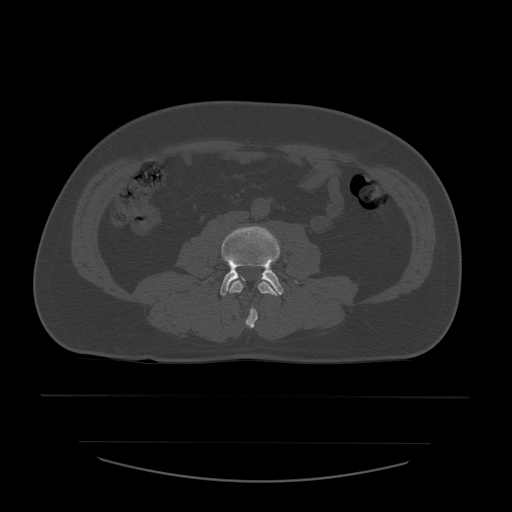
CT including the spine, one axial slice. Slice 157 of 532 in the series (ordered by position). 120 kVp. Bone window (W 1800 / L 400 HU). 1.25 mm slice thickness. 512 × 512 image matrix. Patient age 44 years. From the clinical record (not read from this slice): primary cancer: soft tissue sarcoma.
Outlined on this slice (semi-automatic segmentation, software-assisted and operator-edited):
- L3 vertebra: bounding box (x1, y1, x2, y2) in pixels: (229, 280, 280, 329)
- L4 vertebra: (220, 227, 284, 296)